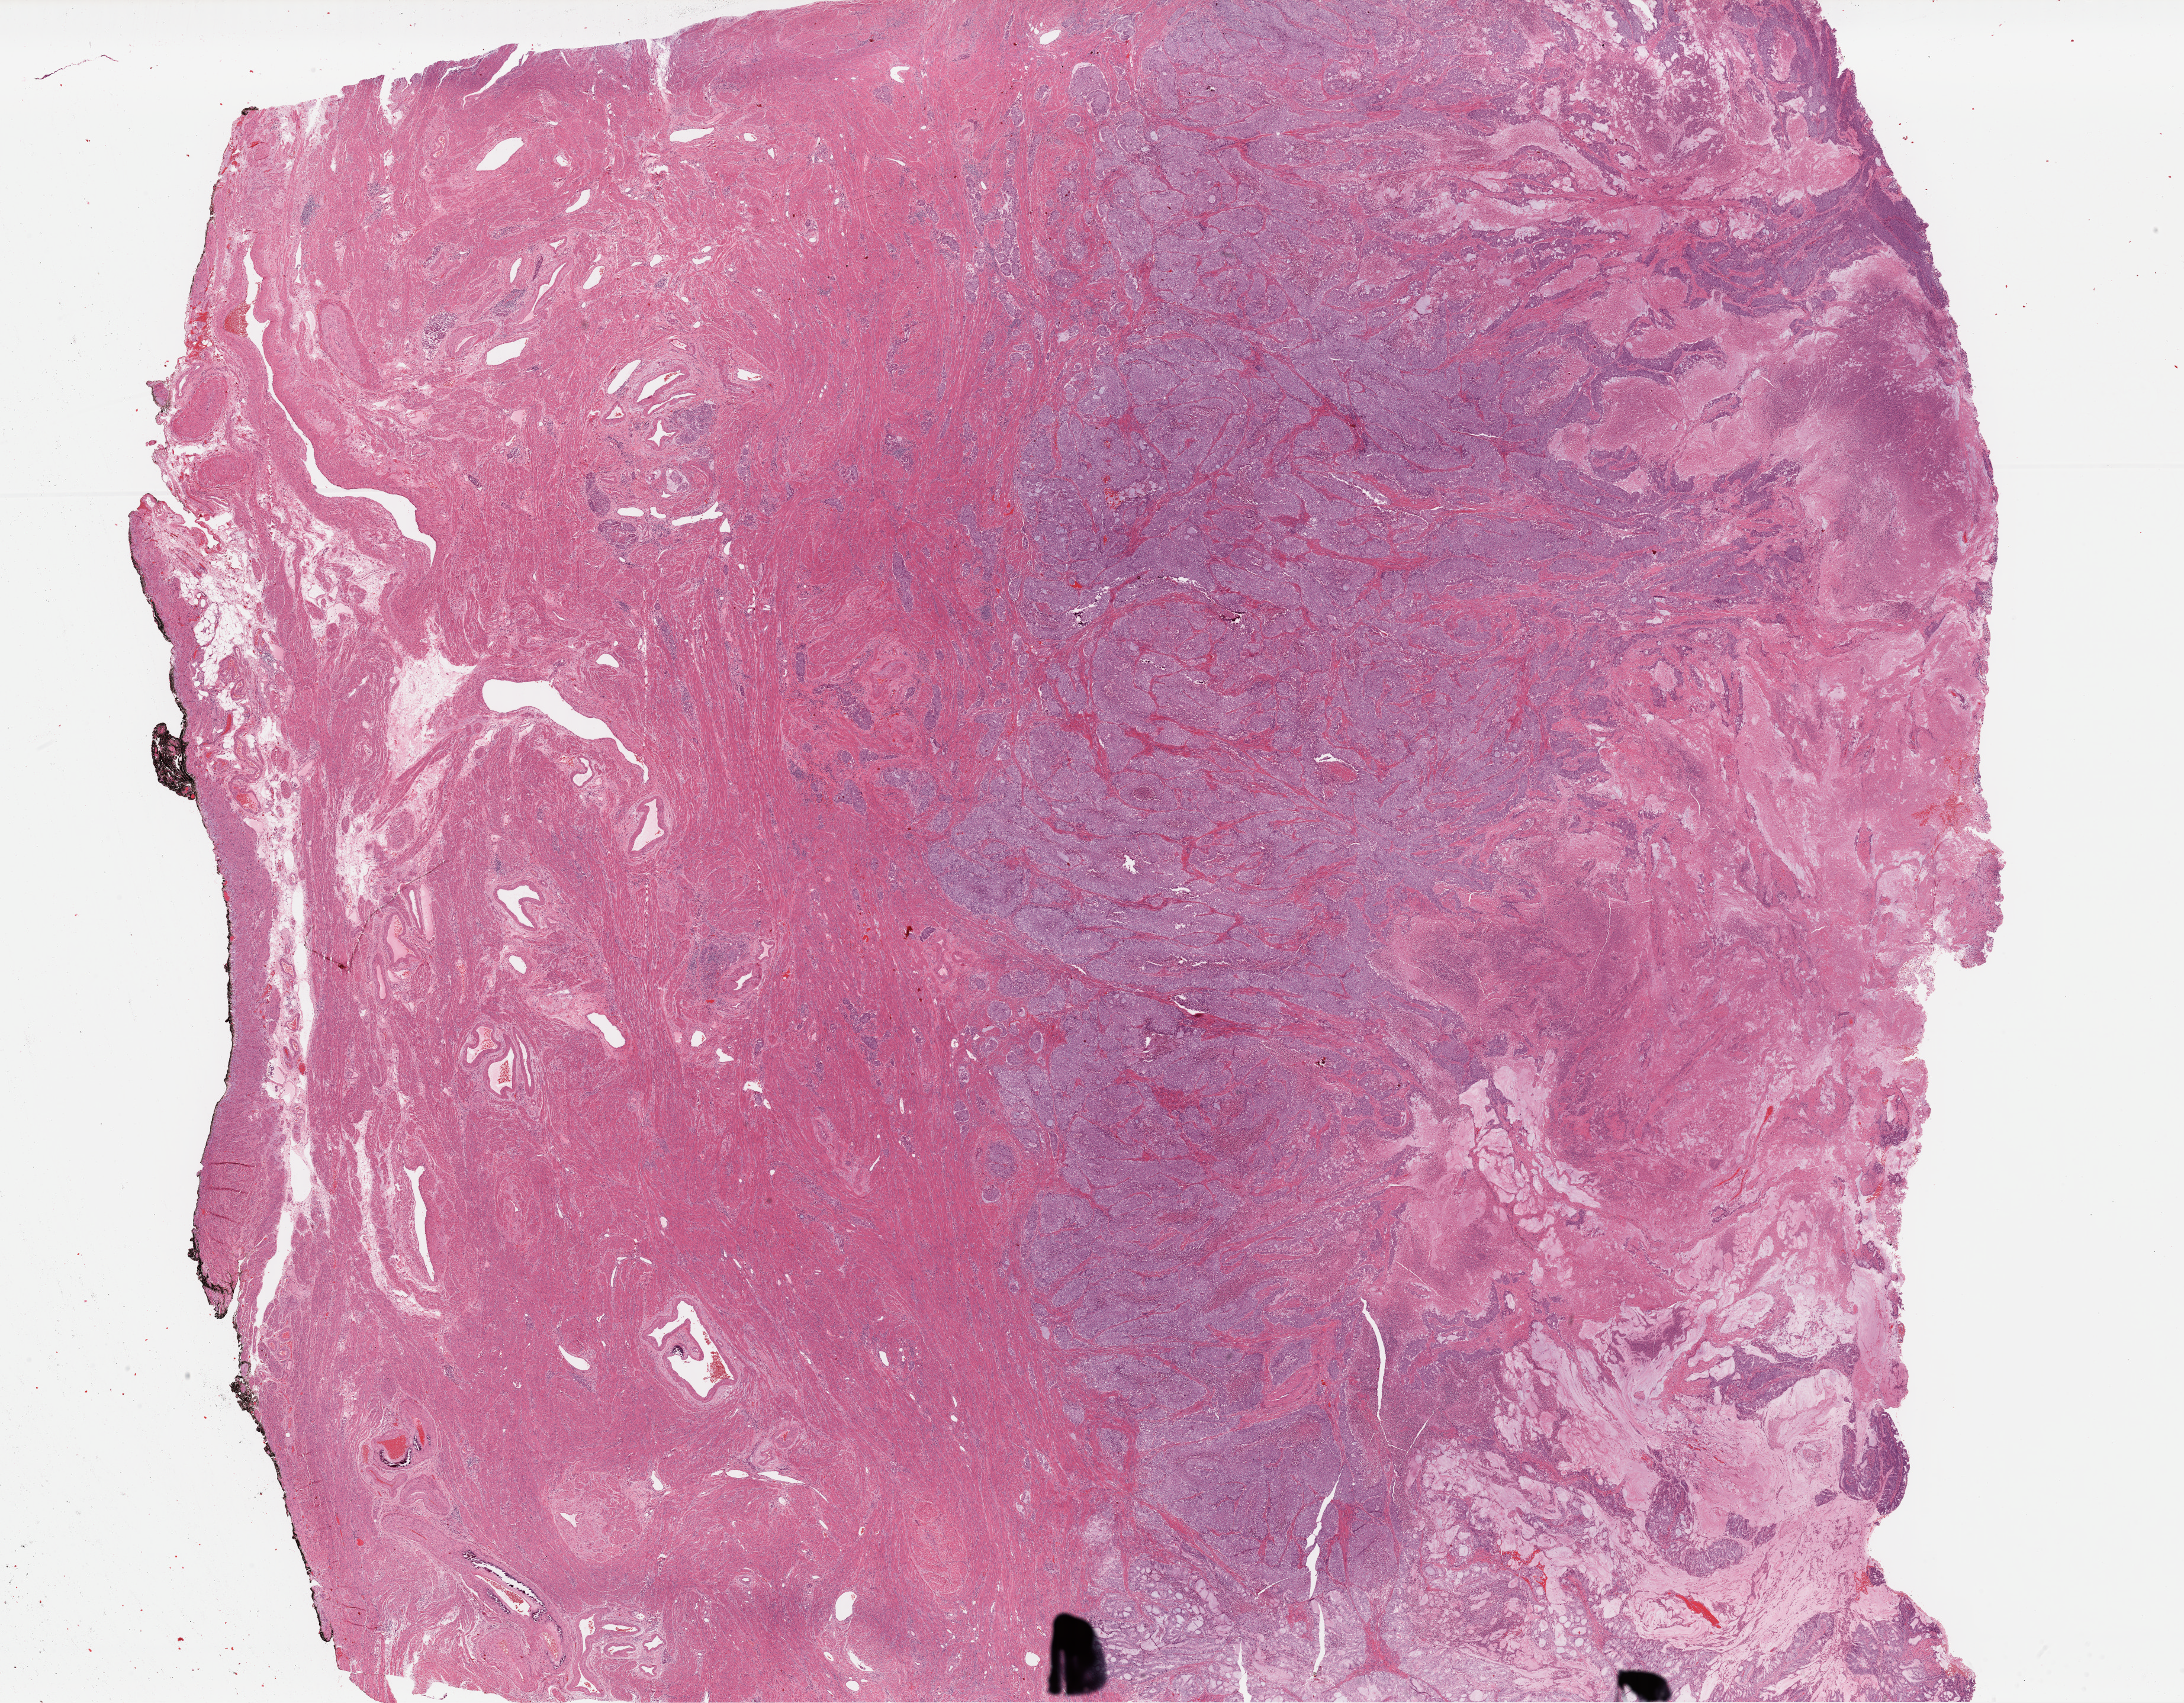
H&E whole-slide image — a low-resolution overview of the entire scanned area, about 29.1 x 22.7 mm, formalin-fixed paraffin-embedded (FFPE) diagnostic section, primary tumour sample from the uterus. Patient: female, age at initial diagnosis 77 years. Histologic grade: G3 (poorly differentiated).
Pathologic diagnosis: Endometrioid adenocarcinoma, NOS. FIGO stage: IC.